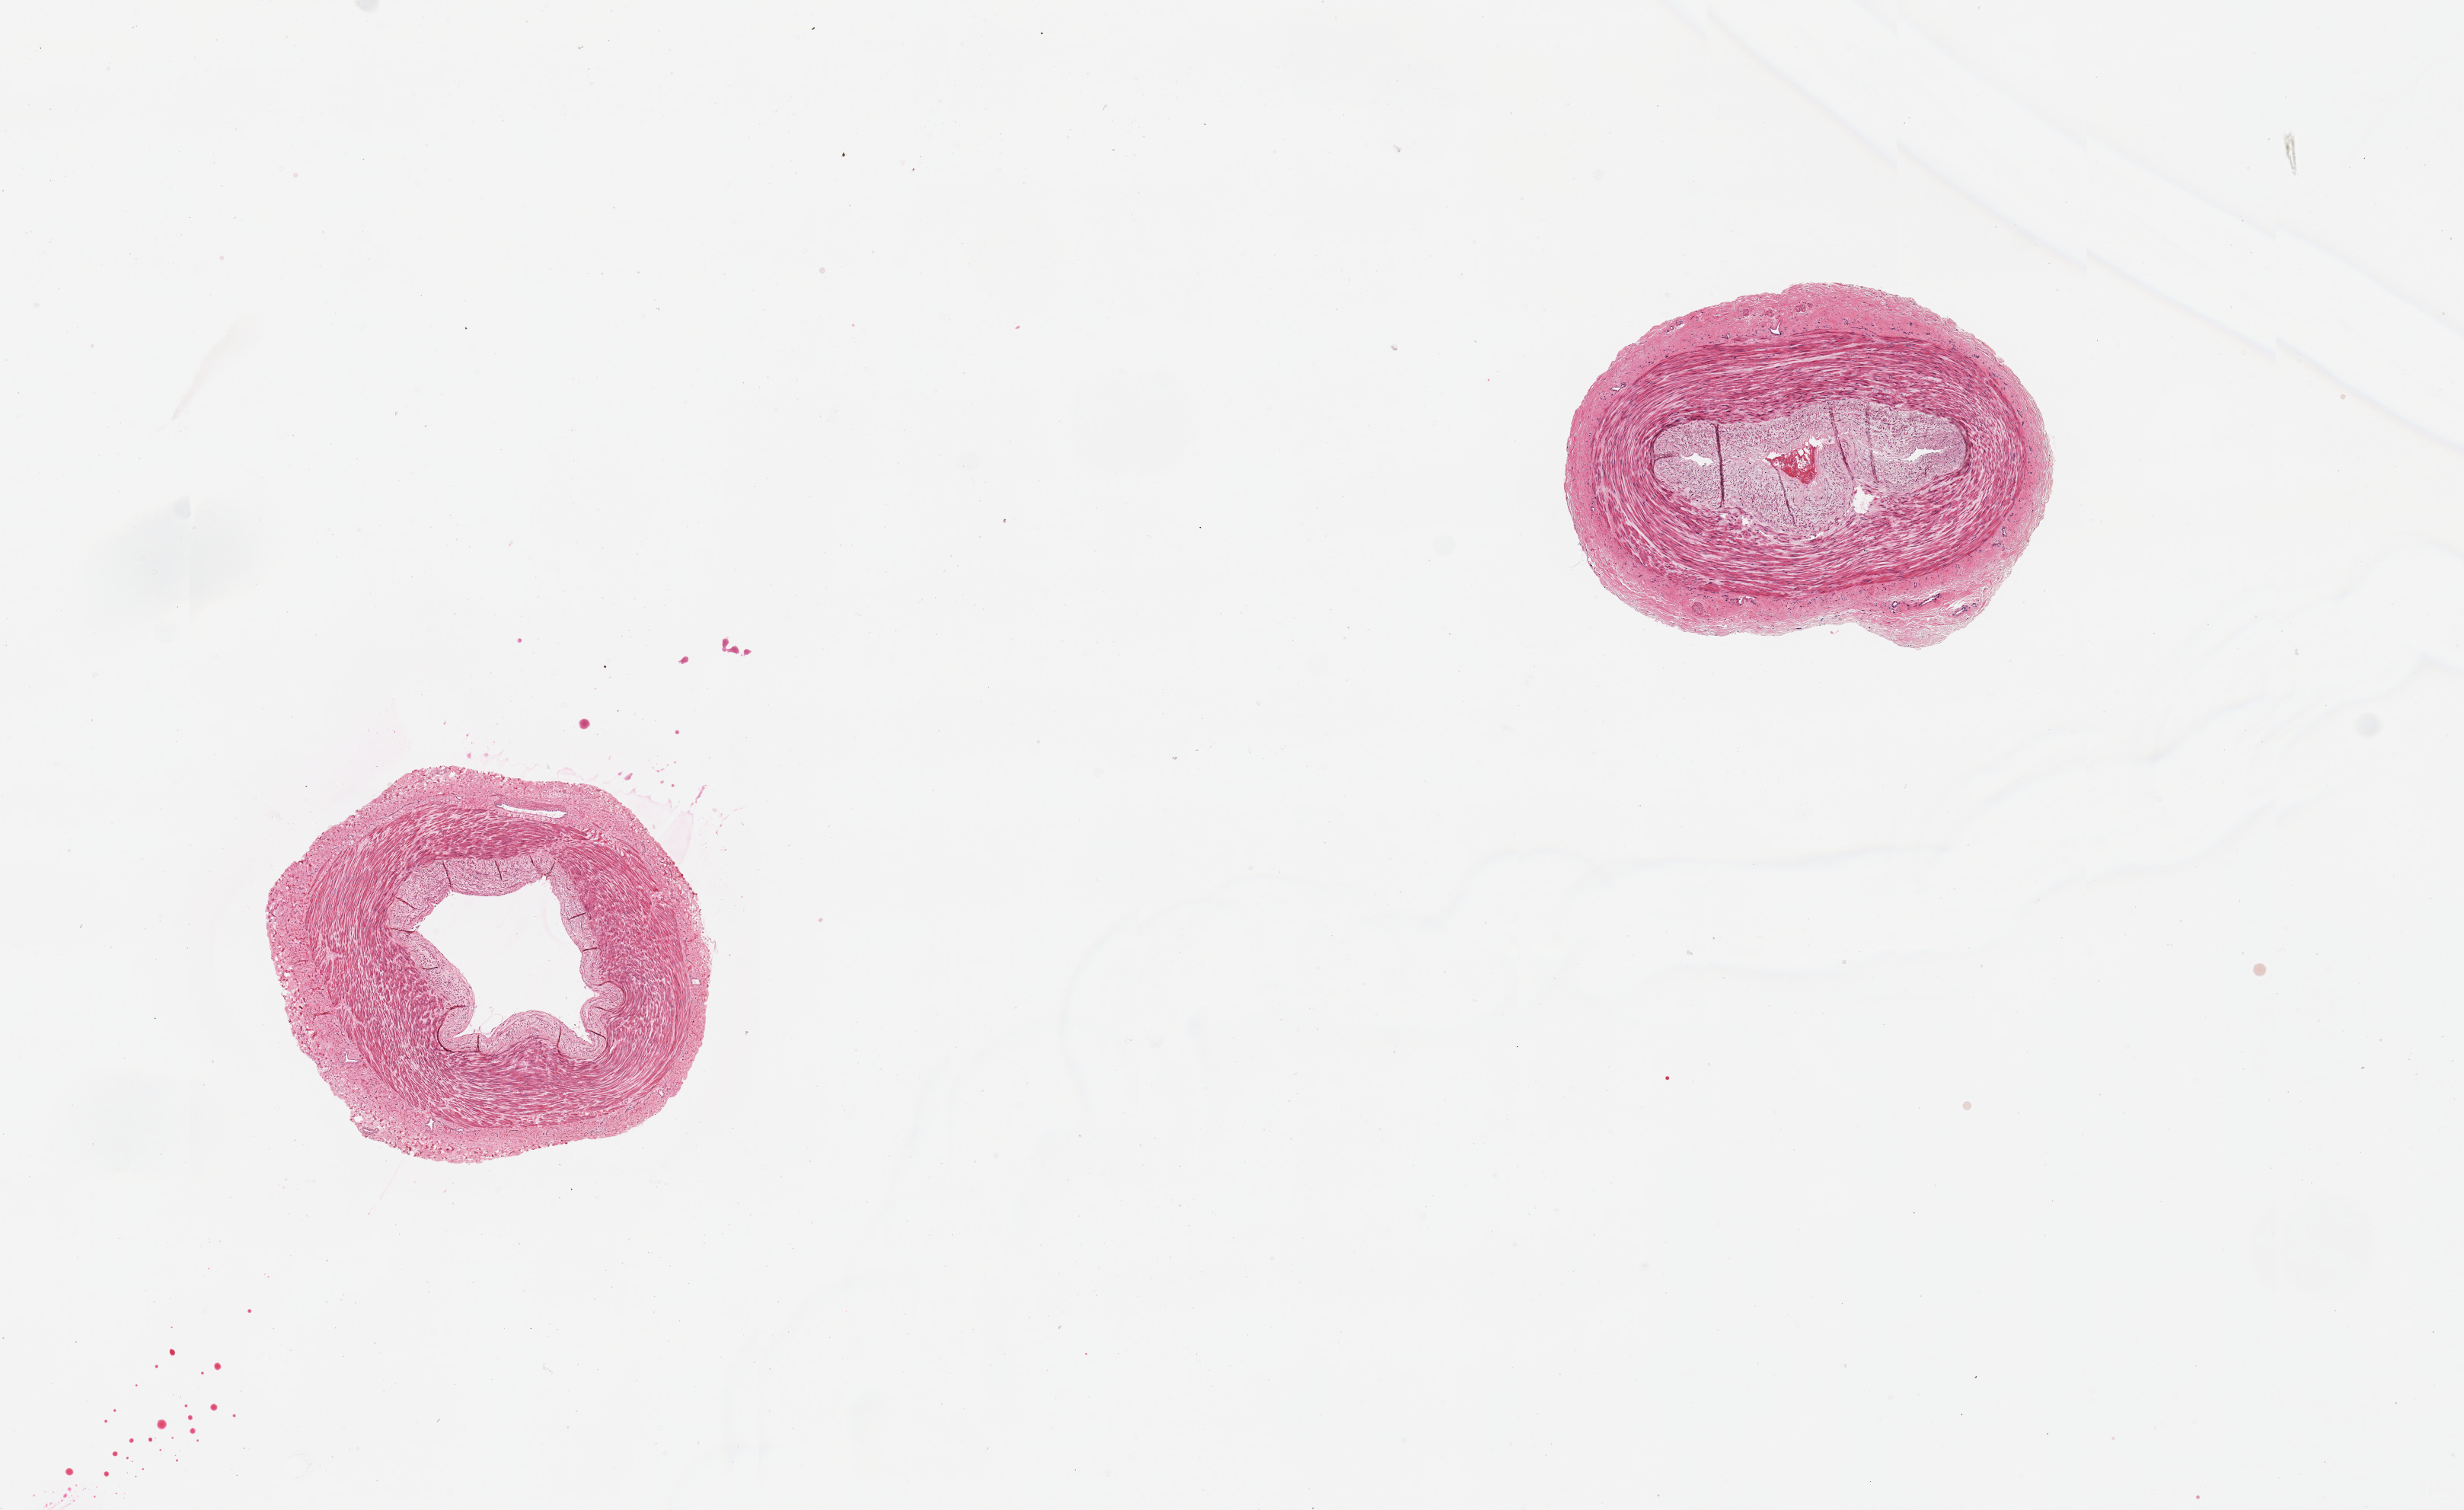
Digitized H&E-stained section, whole scanned area (about 12.8 x 7.8 mm, acquisition: 20x scan) shown as a low-resolution overview. PAXgene-fixed, paraffin-embedded tissue. Target tissue: tibial artery. Donor tissue sample. Male donor.
Pathologist's review note for this sample: 2 pieces, clean sections, no fat.